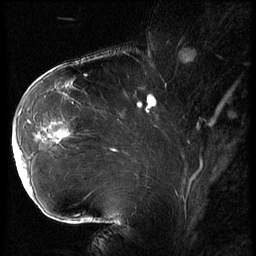
Breast MRI (dynamic contrast-enhanced), one sagittal slice; slice 41 of 62 in the series (ordered by position); 3 images stored at this slice position (order not interpretable as contrast timing); 1.5 T; TE 4.2 ms, TR 9 ms; 2.5 mm slice thickness; 256 × 256 image matrix, field of view 180 × 180 mm. Patient: female, 43 years. Case-level facts recorded for this patient, not image findings: setting: breast cancer imaged before/during neoadjuvant chemotherapy; receptor status: HER2-positive.
Structures marked on this image (semi-automatically segmented with operator editing):
- analysis volume of interest (the breast-tissue region the enhancement analysis was run in; not a lesion): bounding box <13,90,82,203> (left, top, right, bottom; pixels)
- tumour enhancement mask (voxels above the 140 % enhancement threshold inside the analysis volume of interest): <13,125,71,193>